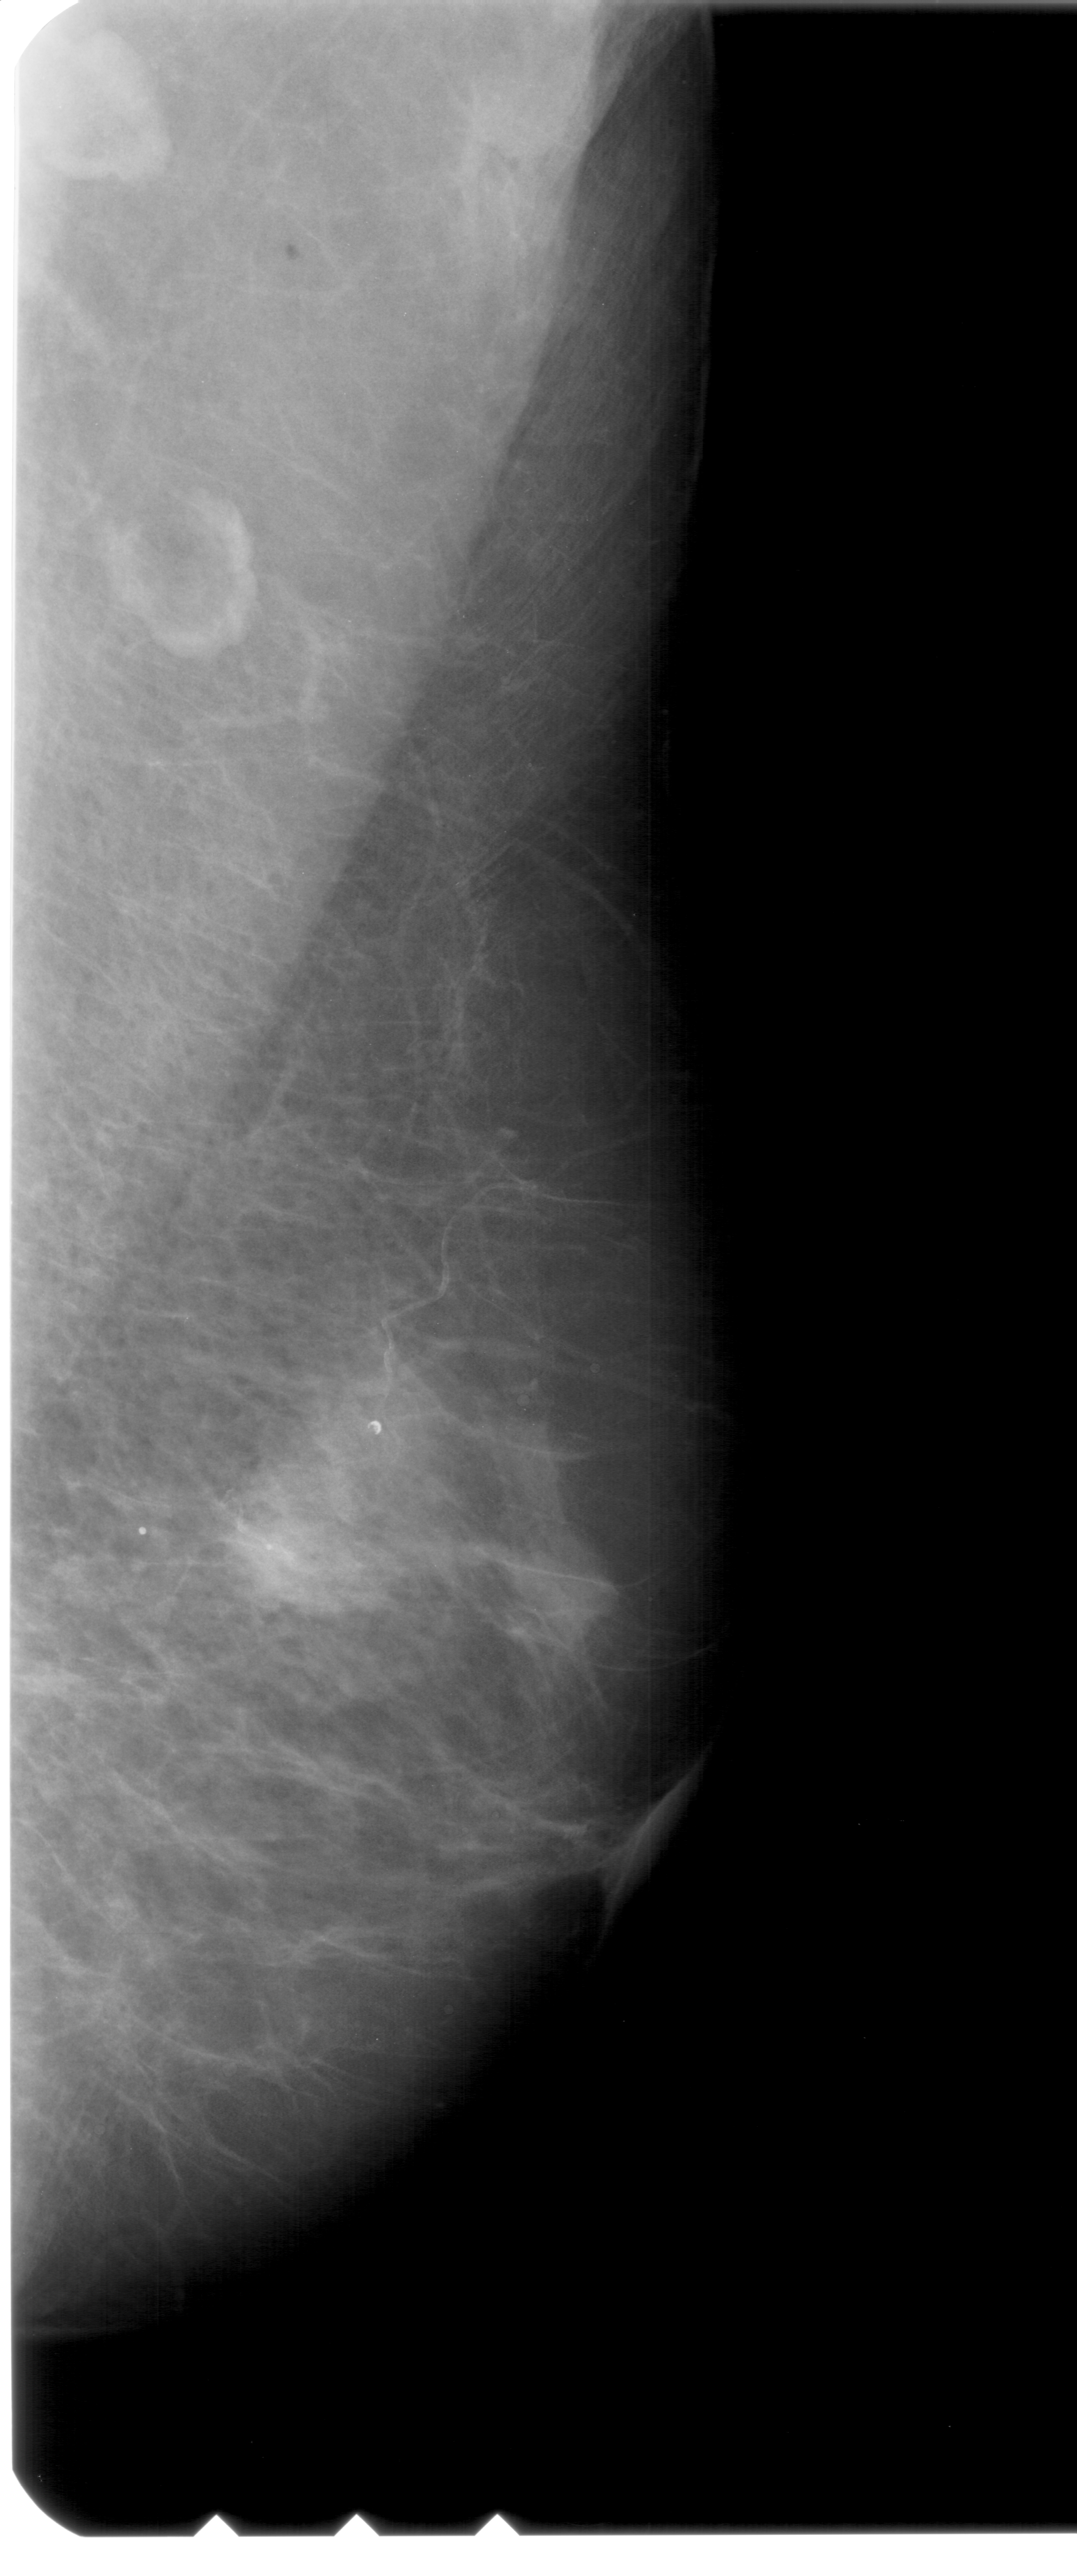
Mammogram (digitized film); right breast; MLO view; BI-RADS breast density category 2 (scale 1–4); 1077 × 2576 image matrix.
Expert-marked regions of interest on this film, with their recorded descriptors:
- Finding 1 of 2: mass, shape oval, margins ill defined; BI-RADS assessment category 4; pathology (as recorded): malignant: bounding box <183,1454,356,1629> (left, top, right, bottom; pixels)
- Finding 2 of 2: mass, shape oval, margins ill defined; BI-RADS assessment category 4; pathology (as recorded): malignant: <489,1527,633,1667>